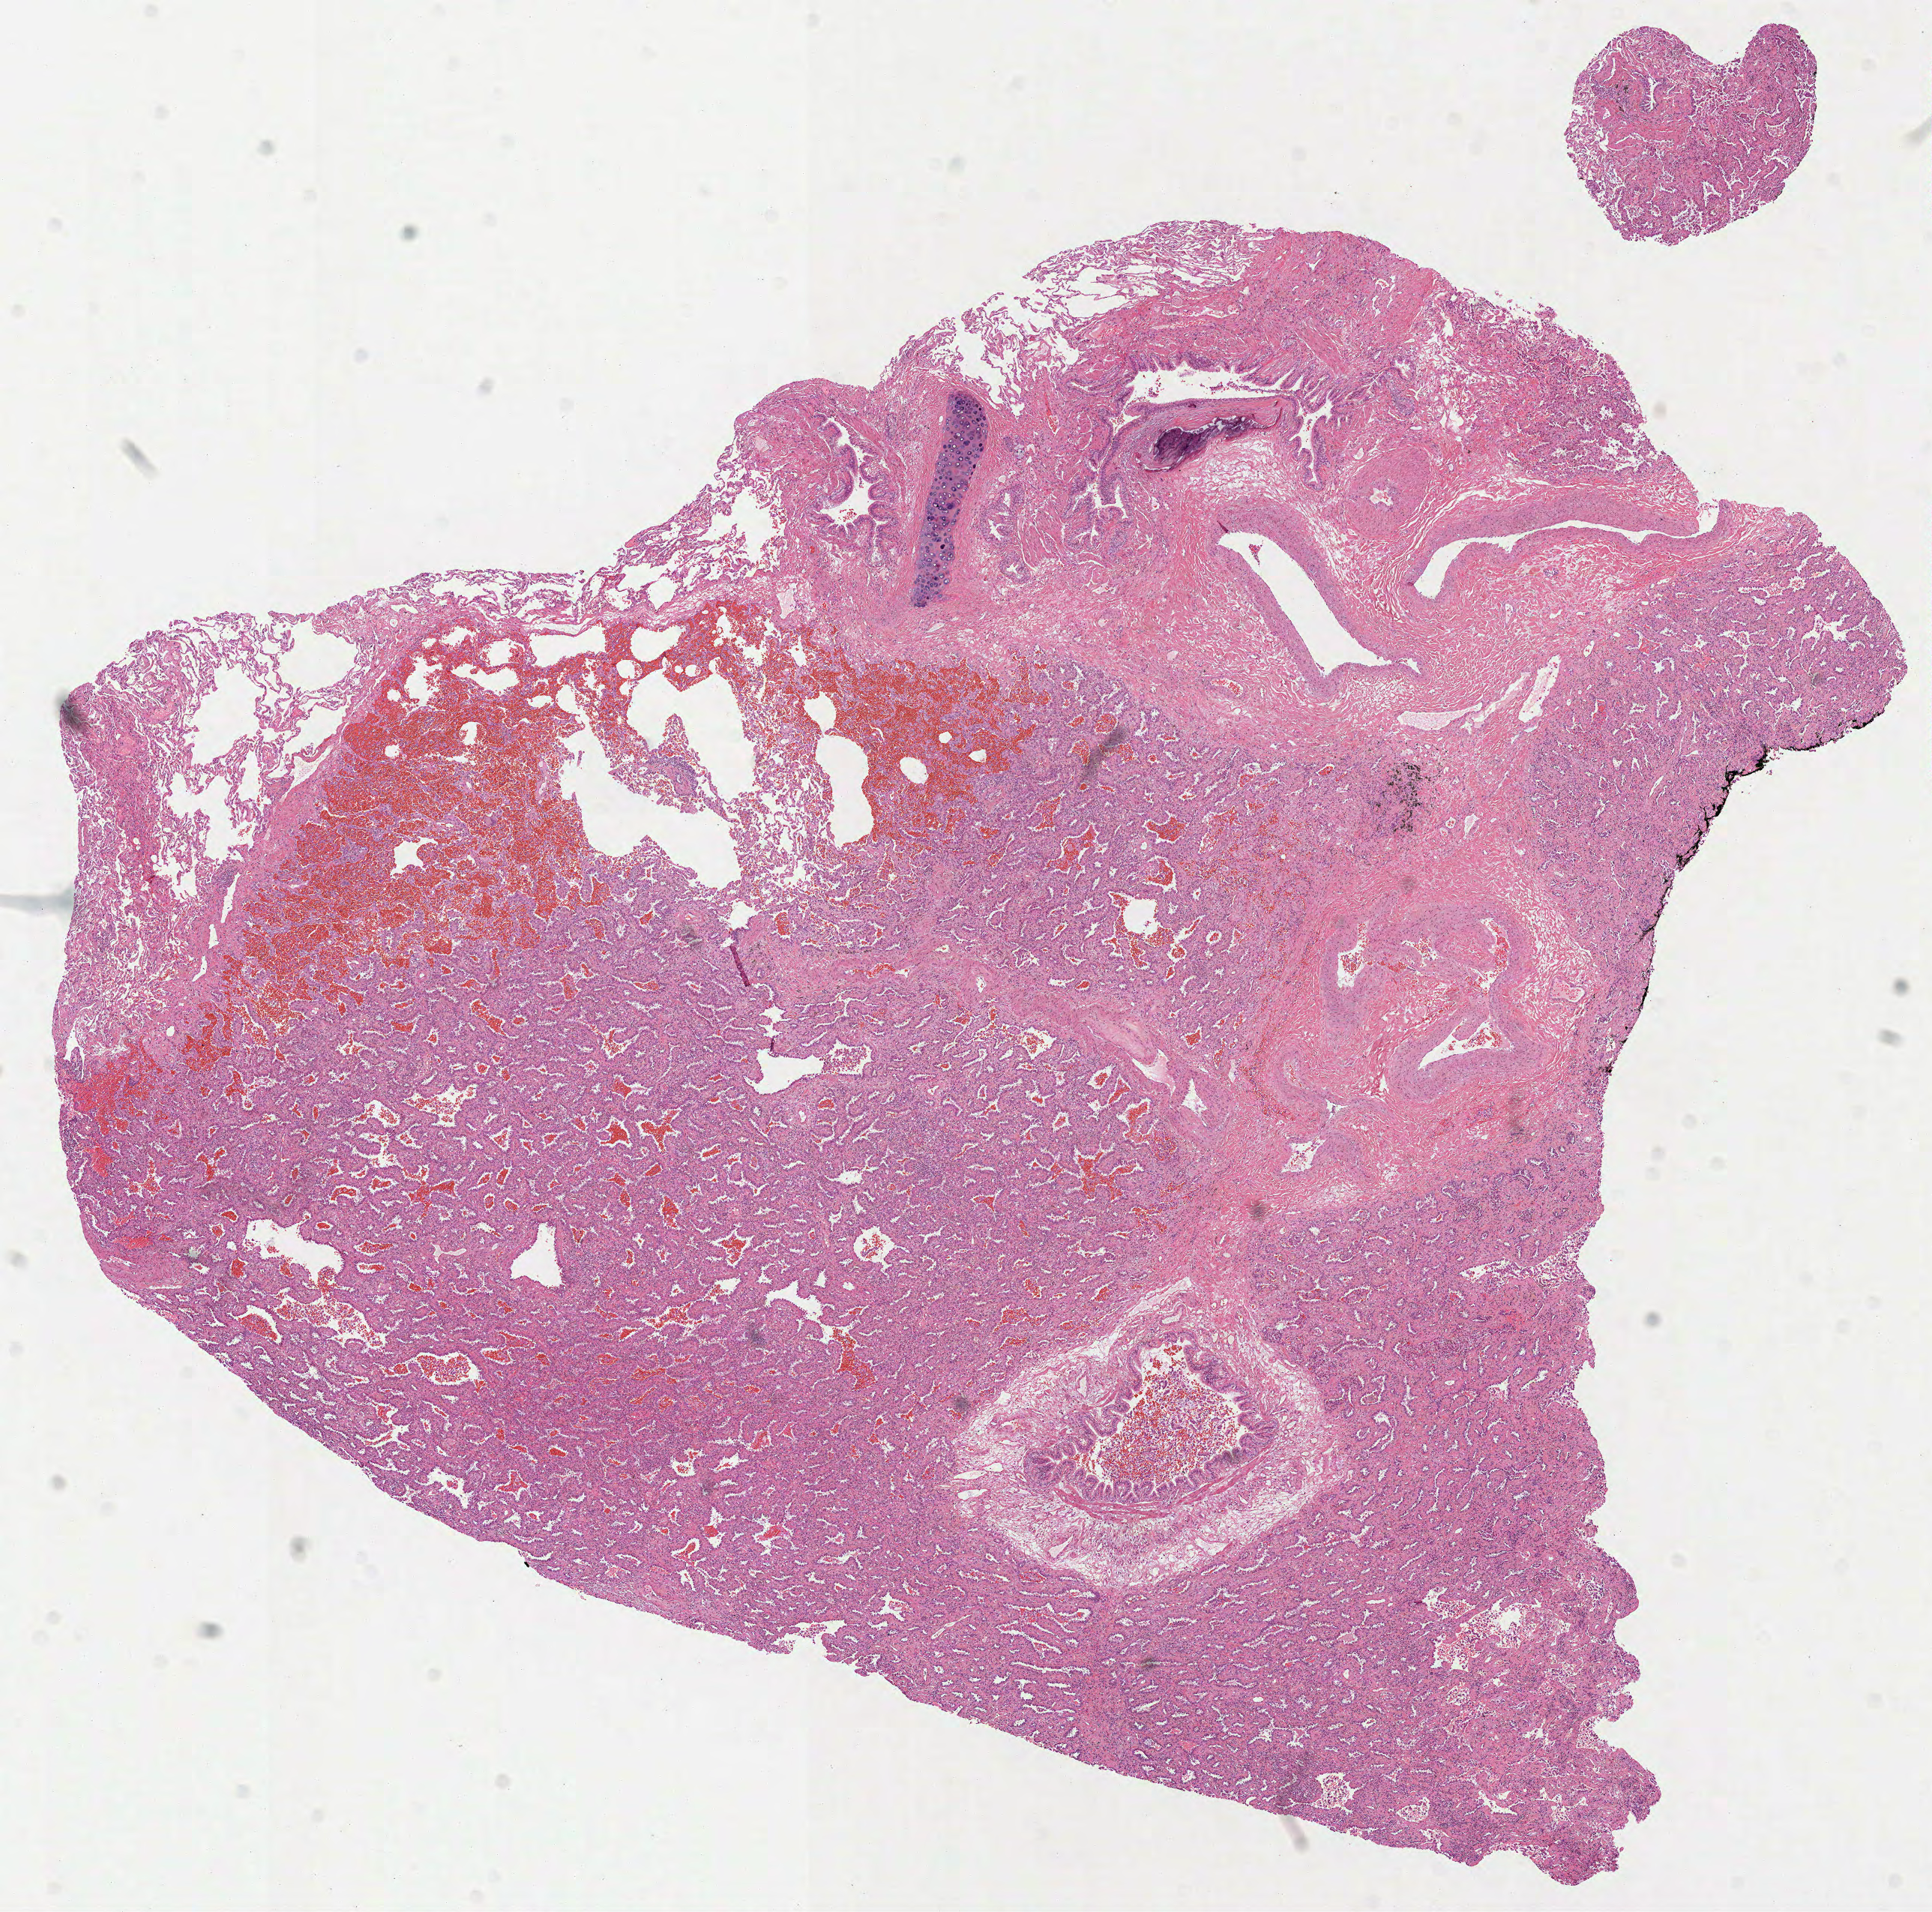
Whole-slide histology image, H&E-stained, shown as a low-resolution overview of the whole scanned area (about 10.4 x 10.3 mm, acquisition: 40x scan), formalin-fixed paraffin-embedded (FFPE) diagnostic section, primary tumour sample from the lung. Male patient; age at initial diagnosis 56 years.
- histologic diagnosis: Adenocarcinoma, NOS (upper lobe, lung)
- AJCC pathologic stage: IA
- laterality: right